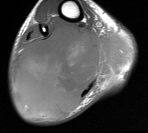
MRI of an extremity soft-tissue mass, one axial slice; MR volume resampled by the dataset authors to the PET/CT grid (not the native acquisition matrix); 3.27 mm slice thickness; 148 × 133 image matrix, field of view 145 × 130 mm. Male patient. Case-level facts recorded for this patient, not image findings: histological type: liposarcoma - round cell; grade: high; site of the primary tumour: right calf.
Structures marked on this image (expert contour drawn on MRI and transferred to this co-registered scan by the dataset authors):
- gross tumour volume (mass): bounding box [x1, y1, x2, y2] px = [13, 23, 132, 116]